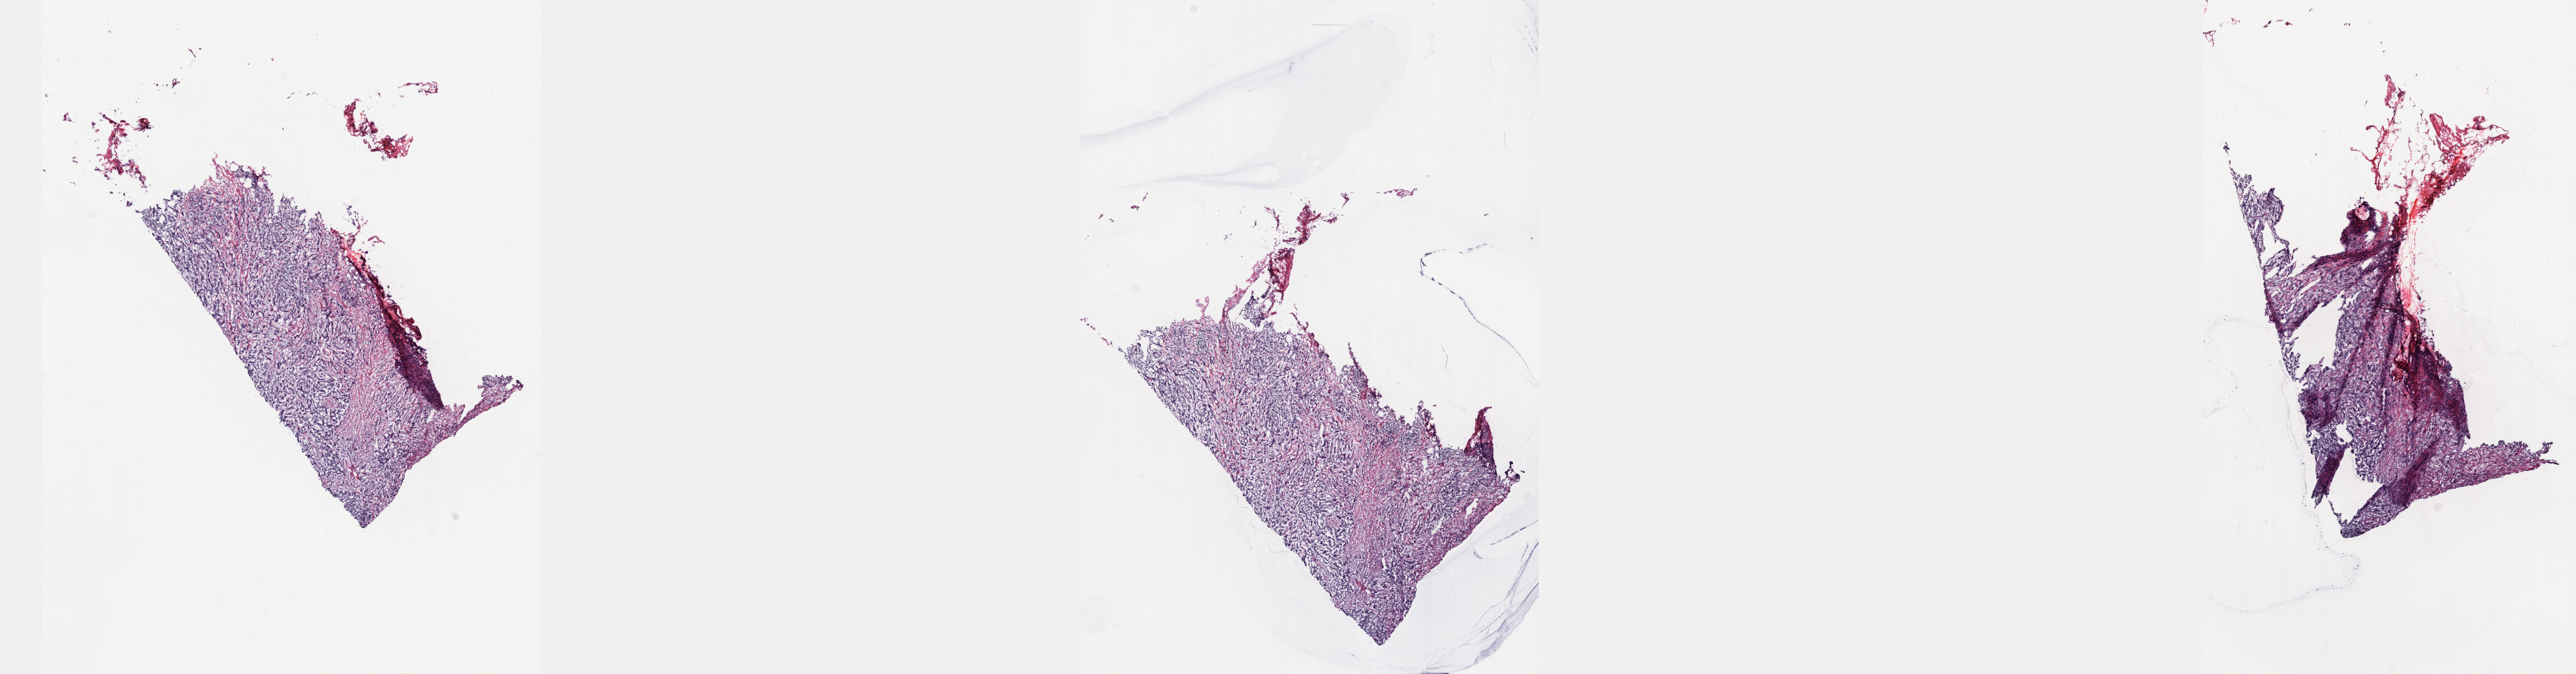
Digitized H&E tissue section (whole slide), shown as a low-resolution overview of the whole scanned area (about 31.2 x 8.2 mm); frozen section; primary tumour sample from the breast. Patient: female, age at initial diagnosis 55 years. Composition of this section per pathologist review: tumour cells 100%, tumour nuclei 75%, normal cells 0%, stromal cells 0%, necrosis 0%. Infiltration values recorded for this section: lymphocyte infiltration 0%, monocyte infiltration 0%, neutrophil infiltration 0%.
- pathologic diagnosis: Infiltrating duct carcinoma, NOS
- AJCC pathologic stage: IIB (7th edition)